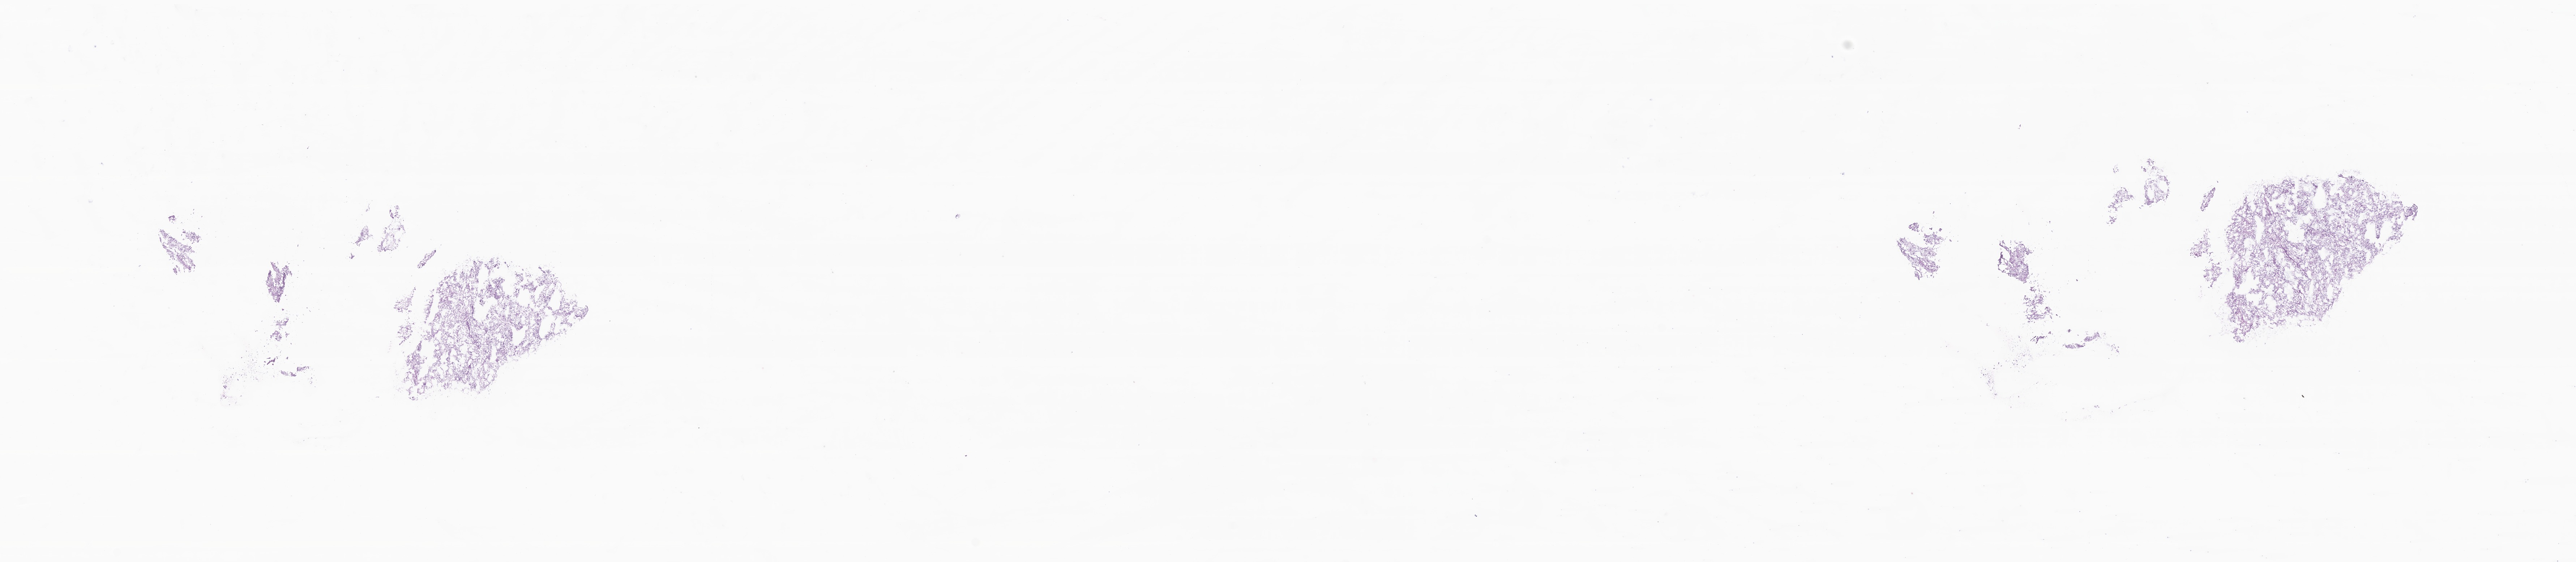
H&E whole-slide image of tumor tissue from the cerebellum, a low-resolution overview of the entire scanned area, about 30.0 x 6.6 mm; frozen section (OCT-embedded). Patient male; age 42 months (3 years 6 months).
Diagnosis: Pilocytic astrocytoma.